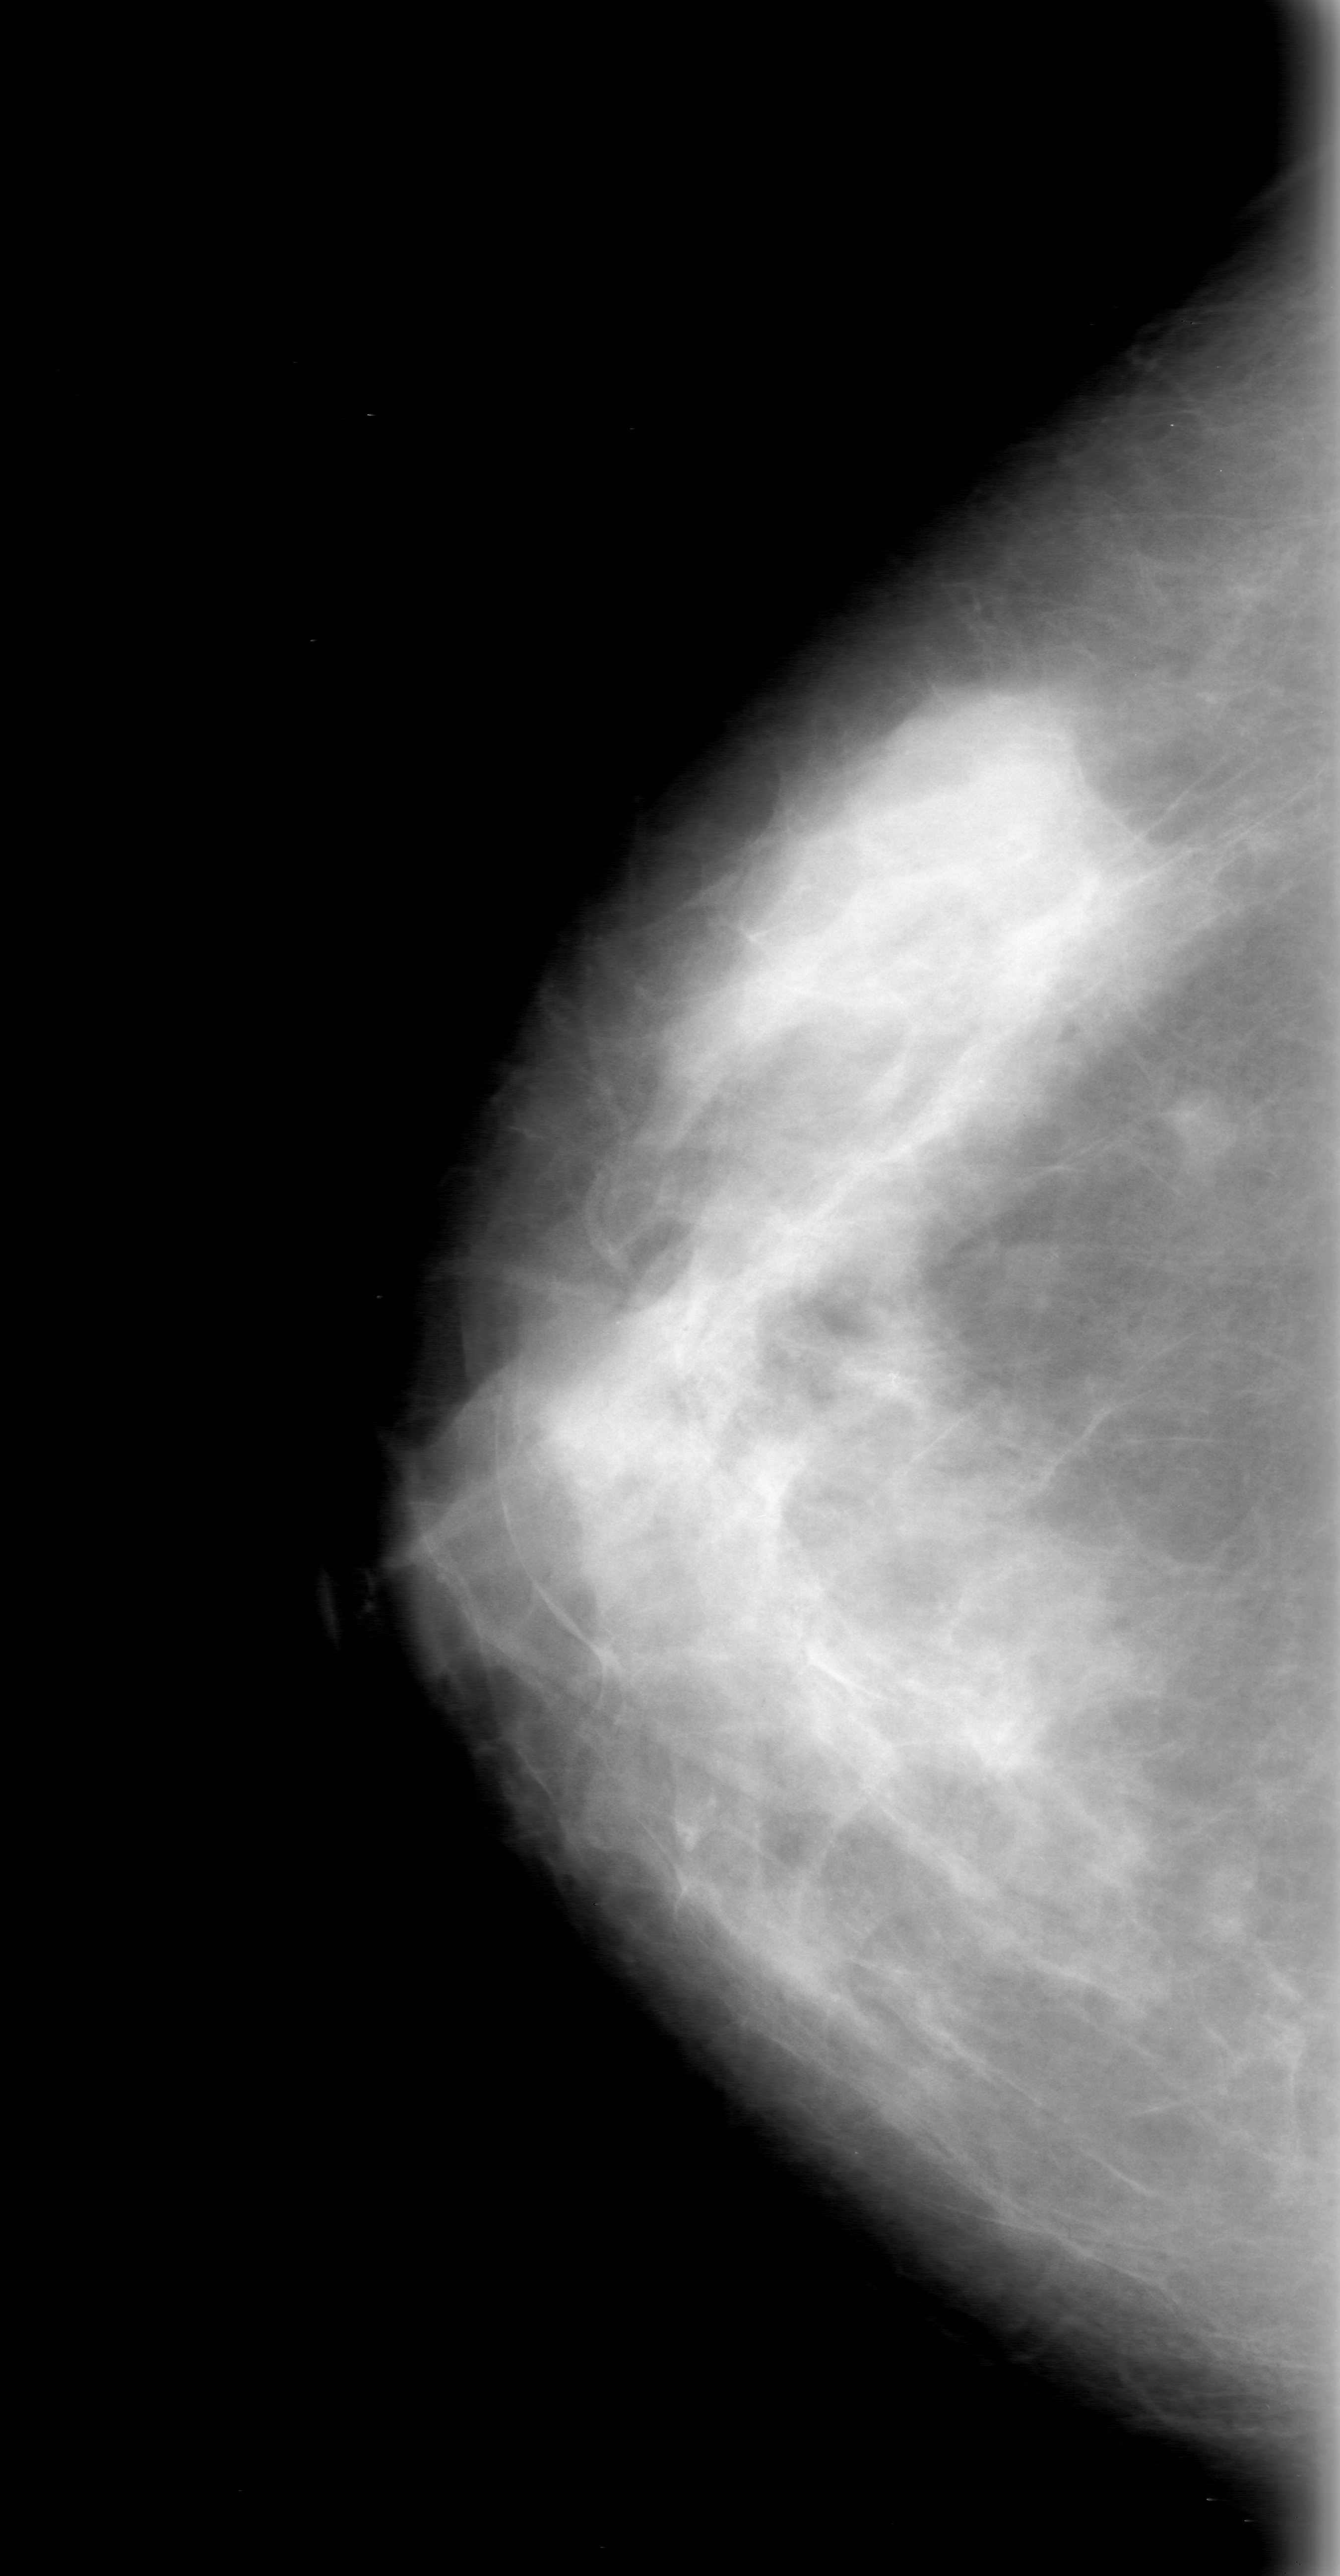
Scanned film-screen mammogram; right breast; craniocaudal (CC) view; 1340 × 2576 image matrix.
Marked abnormalities (boxes around the expert regions of interest):
- calcifications, morphology amorphous, distribution segmental; BI-RADS assessment category 0; subtlety rating 3 on a 1 (subtle) to 5 (obvious) scale; pathology result (as recorded, not read from the image): benign: bounding box [x1, y1, x2, y2] px = [820, 1307, 956, 1457]